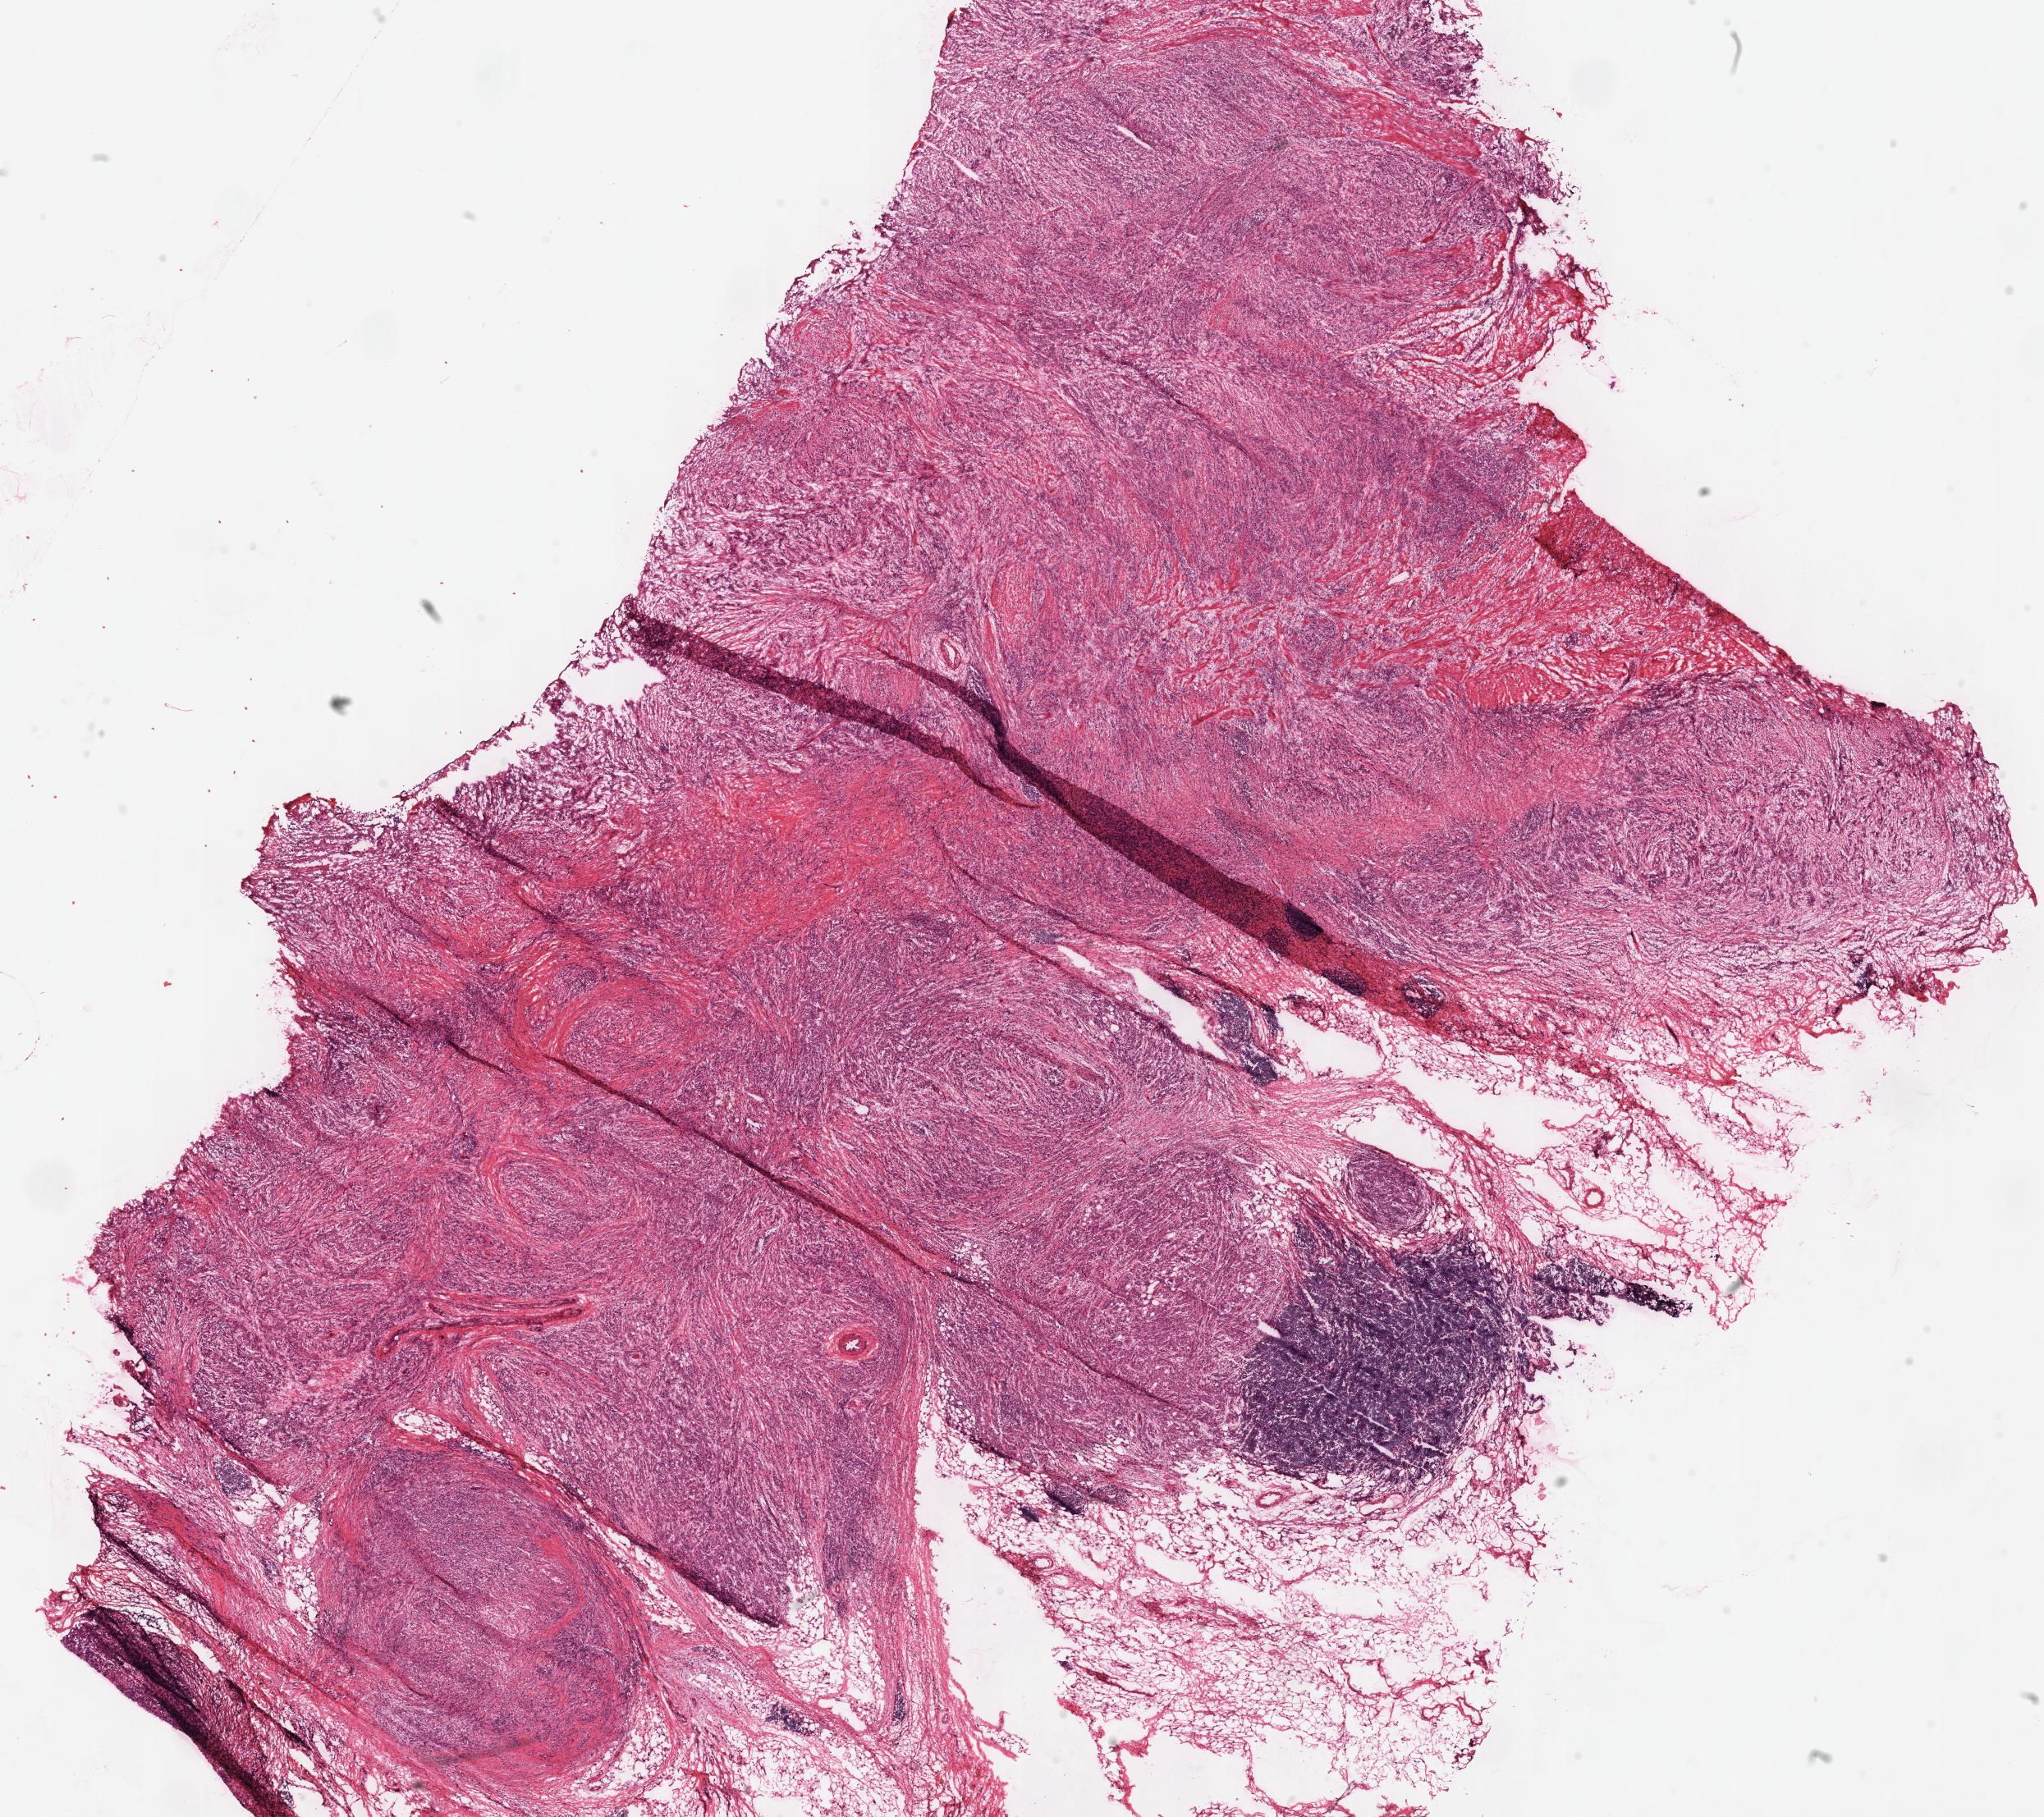
Digitized Hematoxylin and eosin (H&E) stained tissue section (whole slide), low-resolution overview of the scanned area, about 19.6 x 17.4 mm (from a 40x scan). Frozen section. Primary tumour sample from the stomach. Female patient; age at initial diagnosis 80 years. Histologic grade: G3 (poorly differentiated). Composition of this section per pathologist review: tumour cells 85%, tumour nuclei 75%, normal cells 0%, stromal cells 15%, necrosis 0%.
Pathologic diagnosis: Adenocarcinoma, NOS (fundus of stomach). AJCC pathologic stage: IIA (7th edition). Lymph nodes positive (case pathology): 0 of 15 examined.